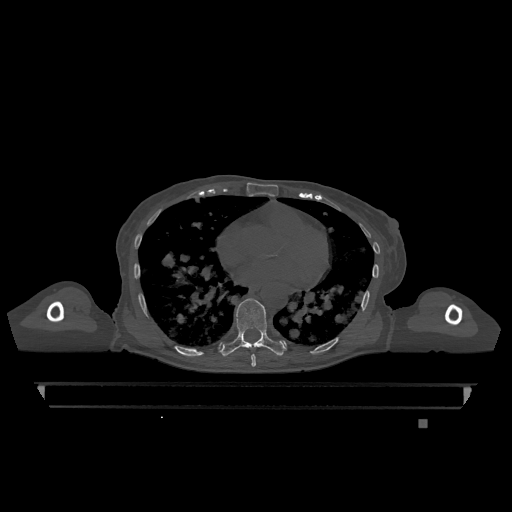
CT including the spine, one axial slice; position 698 of 1317 along the scan axis; bone window (W 1800 / L 400 HU); 512 × 512 image matrix, field of view 500 × 500 mm. Female patient, age 74 years. Case-level facts recorded for this patient, not image findings: primary cancer: lung.
Outlined on this slice (semi-automatic segmentation, software-assisted and operator-edited):
- T7 vertebra: bounding box (x1, y1, x2, y2) in pixels: (251, 354, 256, 367)
- T9 vertebra: (221, 298, 284, 357)